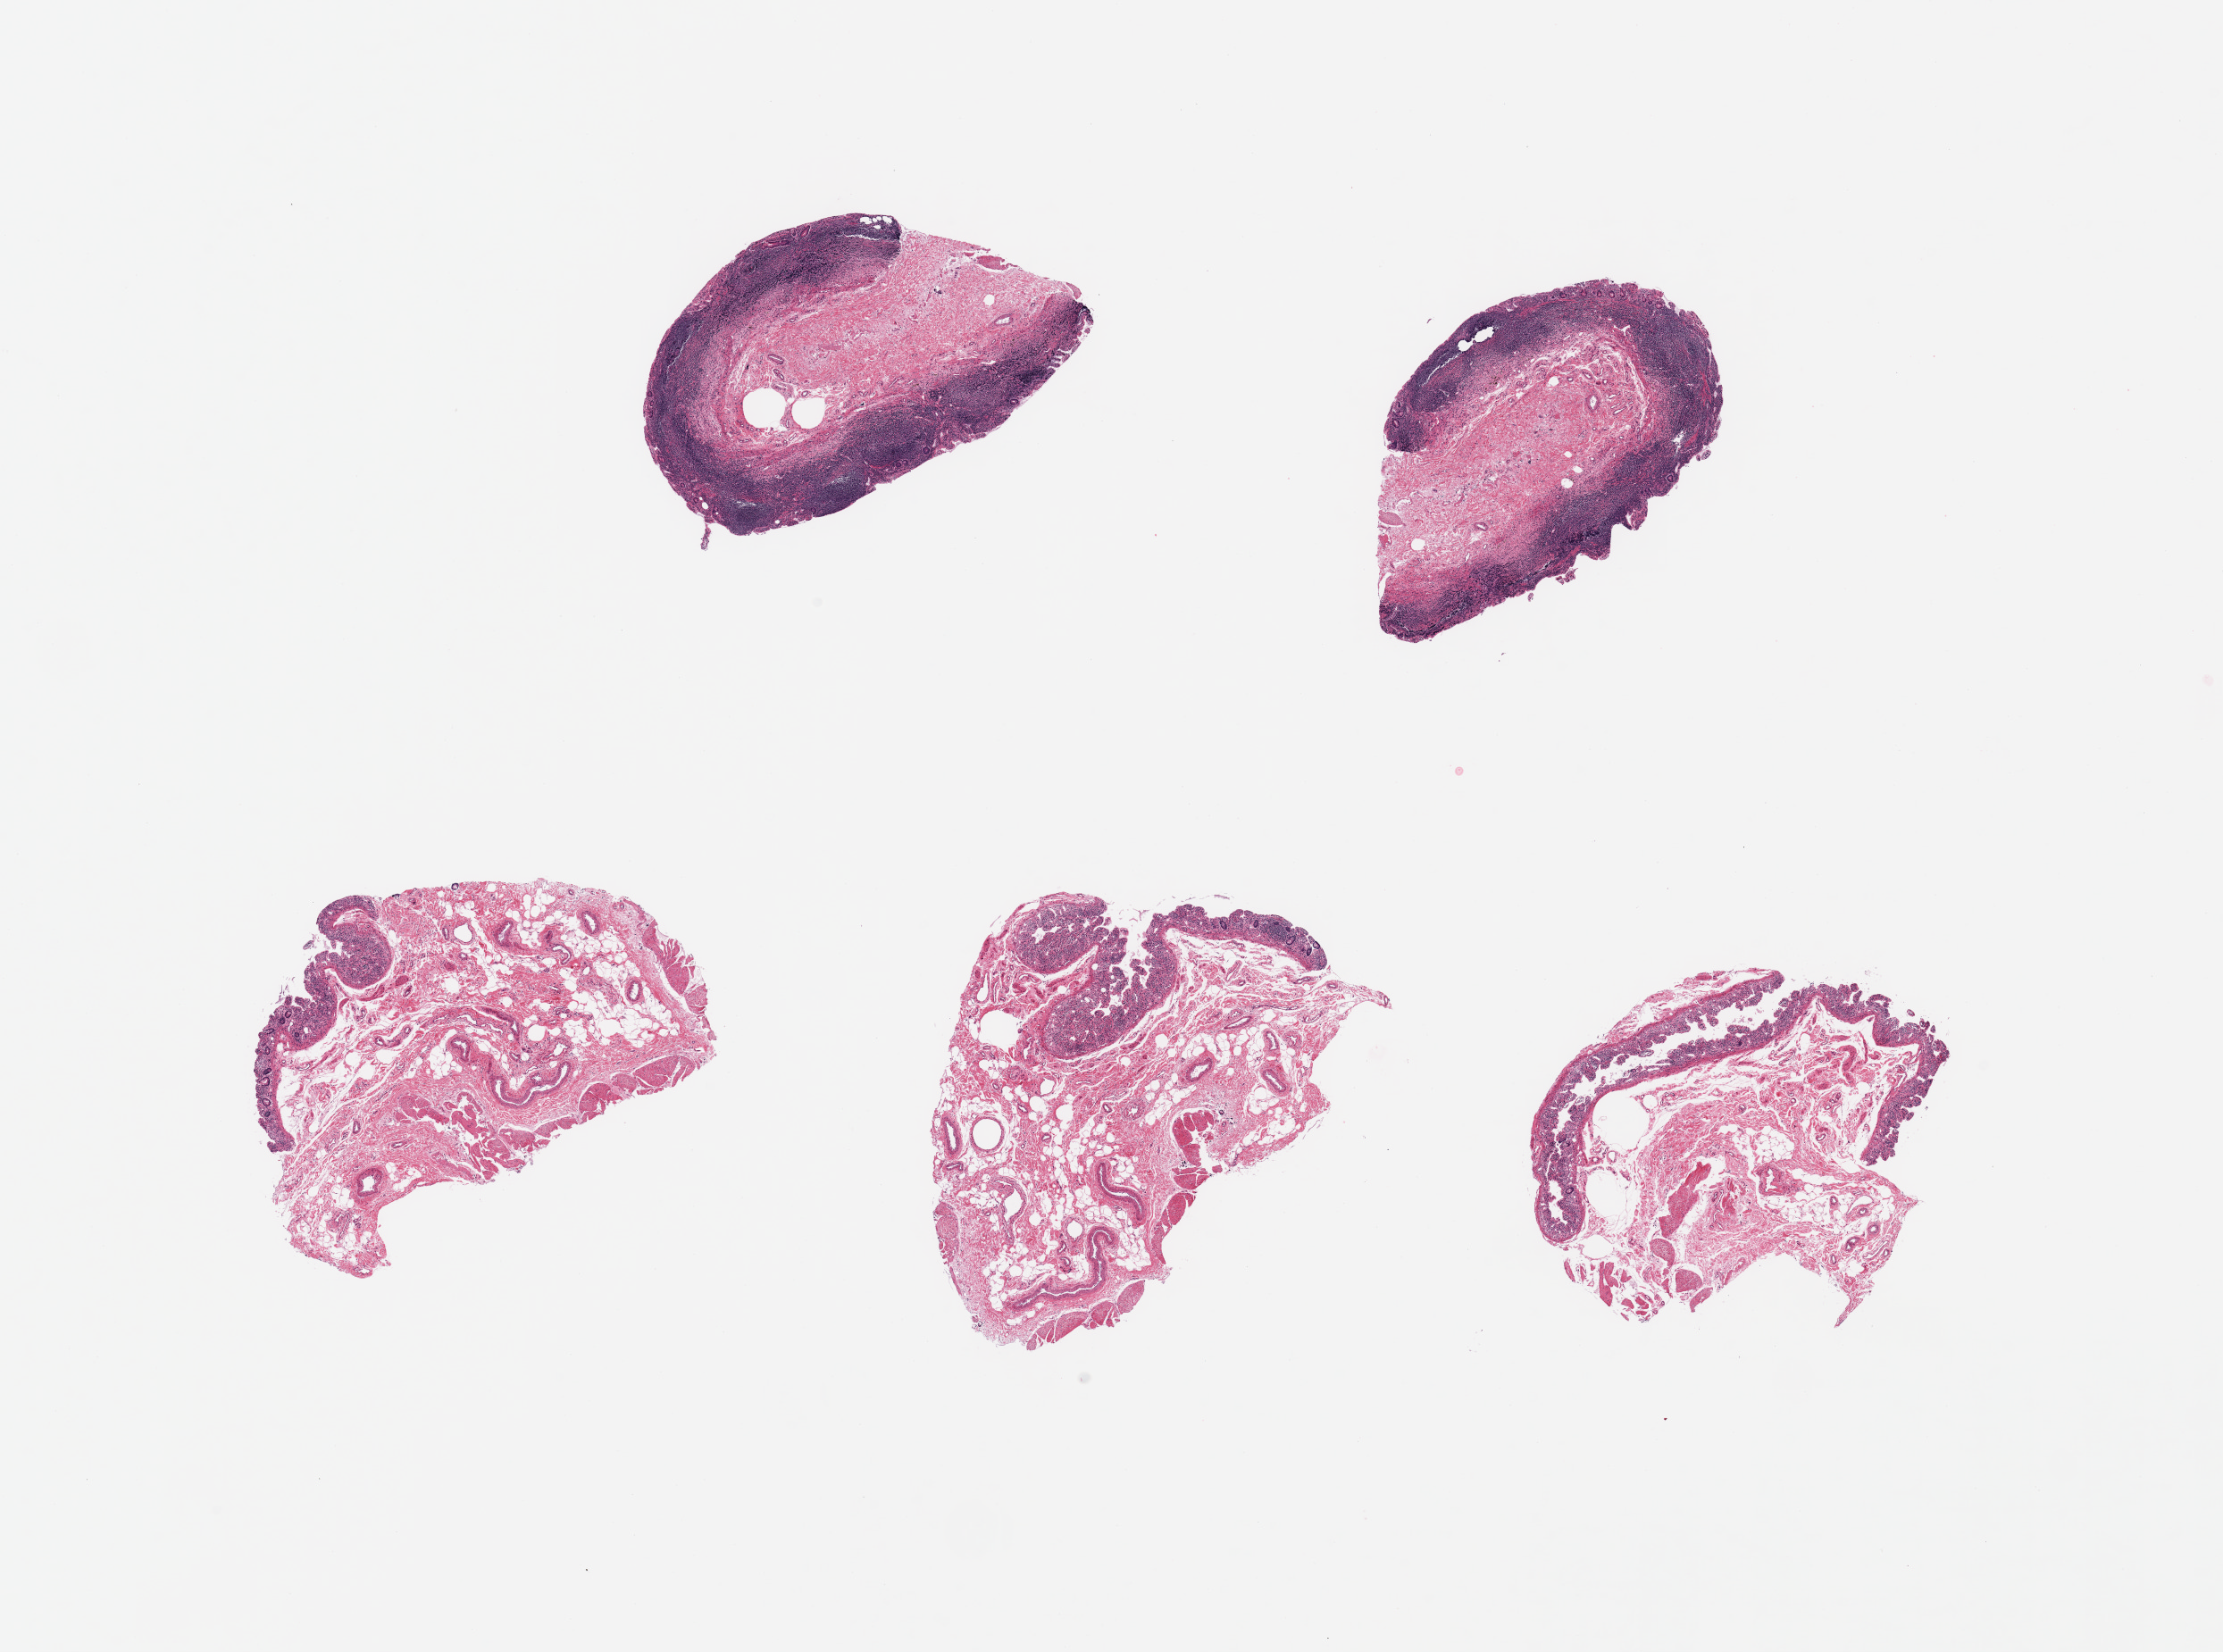
Whole-slide image, H&E stain — whole scanned area (about 19.7 x 14.6 mm) shown as a low-resolution overview; PAXgene-fixed, paraffin-embedded tissue; target tissue: ileum; donor tissue sample. Donor: female.
Reviewer comment on this tissue sample: 6 pieces; autolyzed mucosa; at least 50% of tissue are residual target lymphoid aggregates.